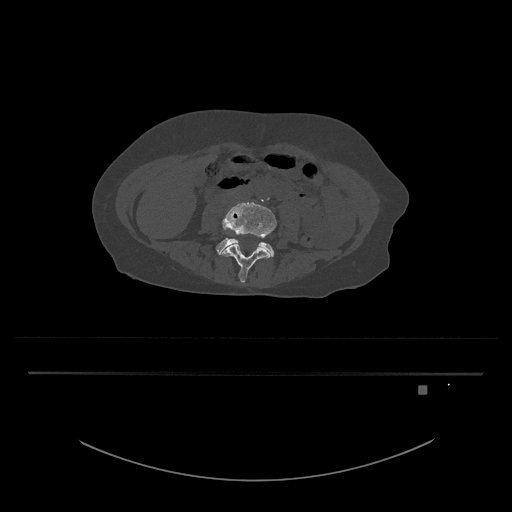
CT including the spine, one axial slice. Position 343 of 797 along the scan axis. Reconstruction kernel Br40s/3. Bone window (W 1800 / L 400 HU). 0.5 mm slice thickness. 512 × 512 image matrix, field of view 500 × 500 mm. Female patient, age 57 years. Case-level facts recorded for this patient, not image findings: primary cancer: cervical.
Structures marked on this image (semi-automatic segmentation, software-assisted and operator-edited):
- L4 vertebra: bounding box <219,202,277,283> (left, top, right, bottom; pixels)